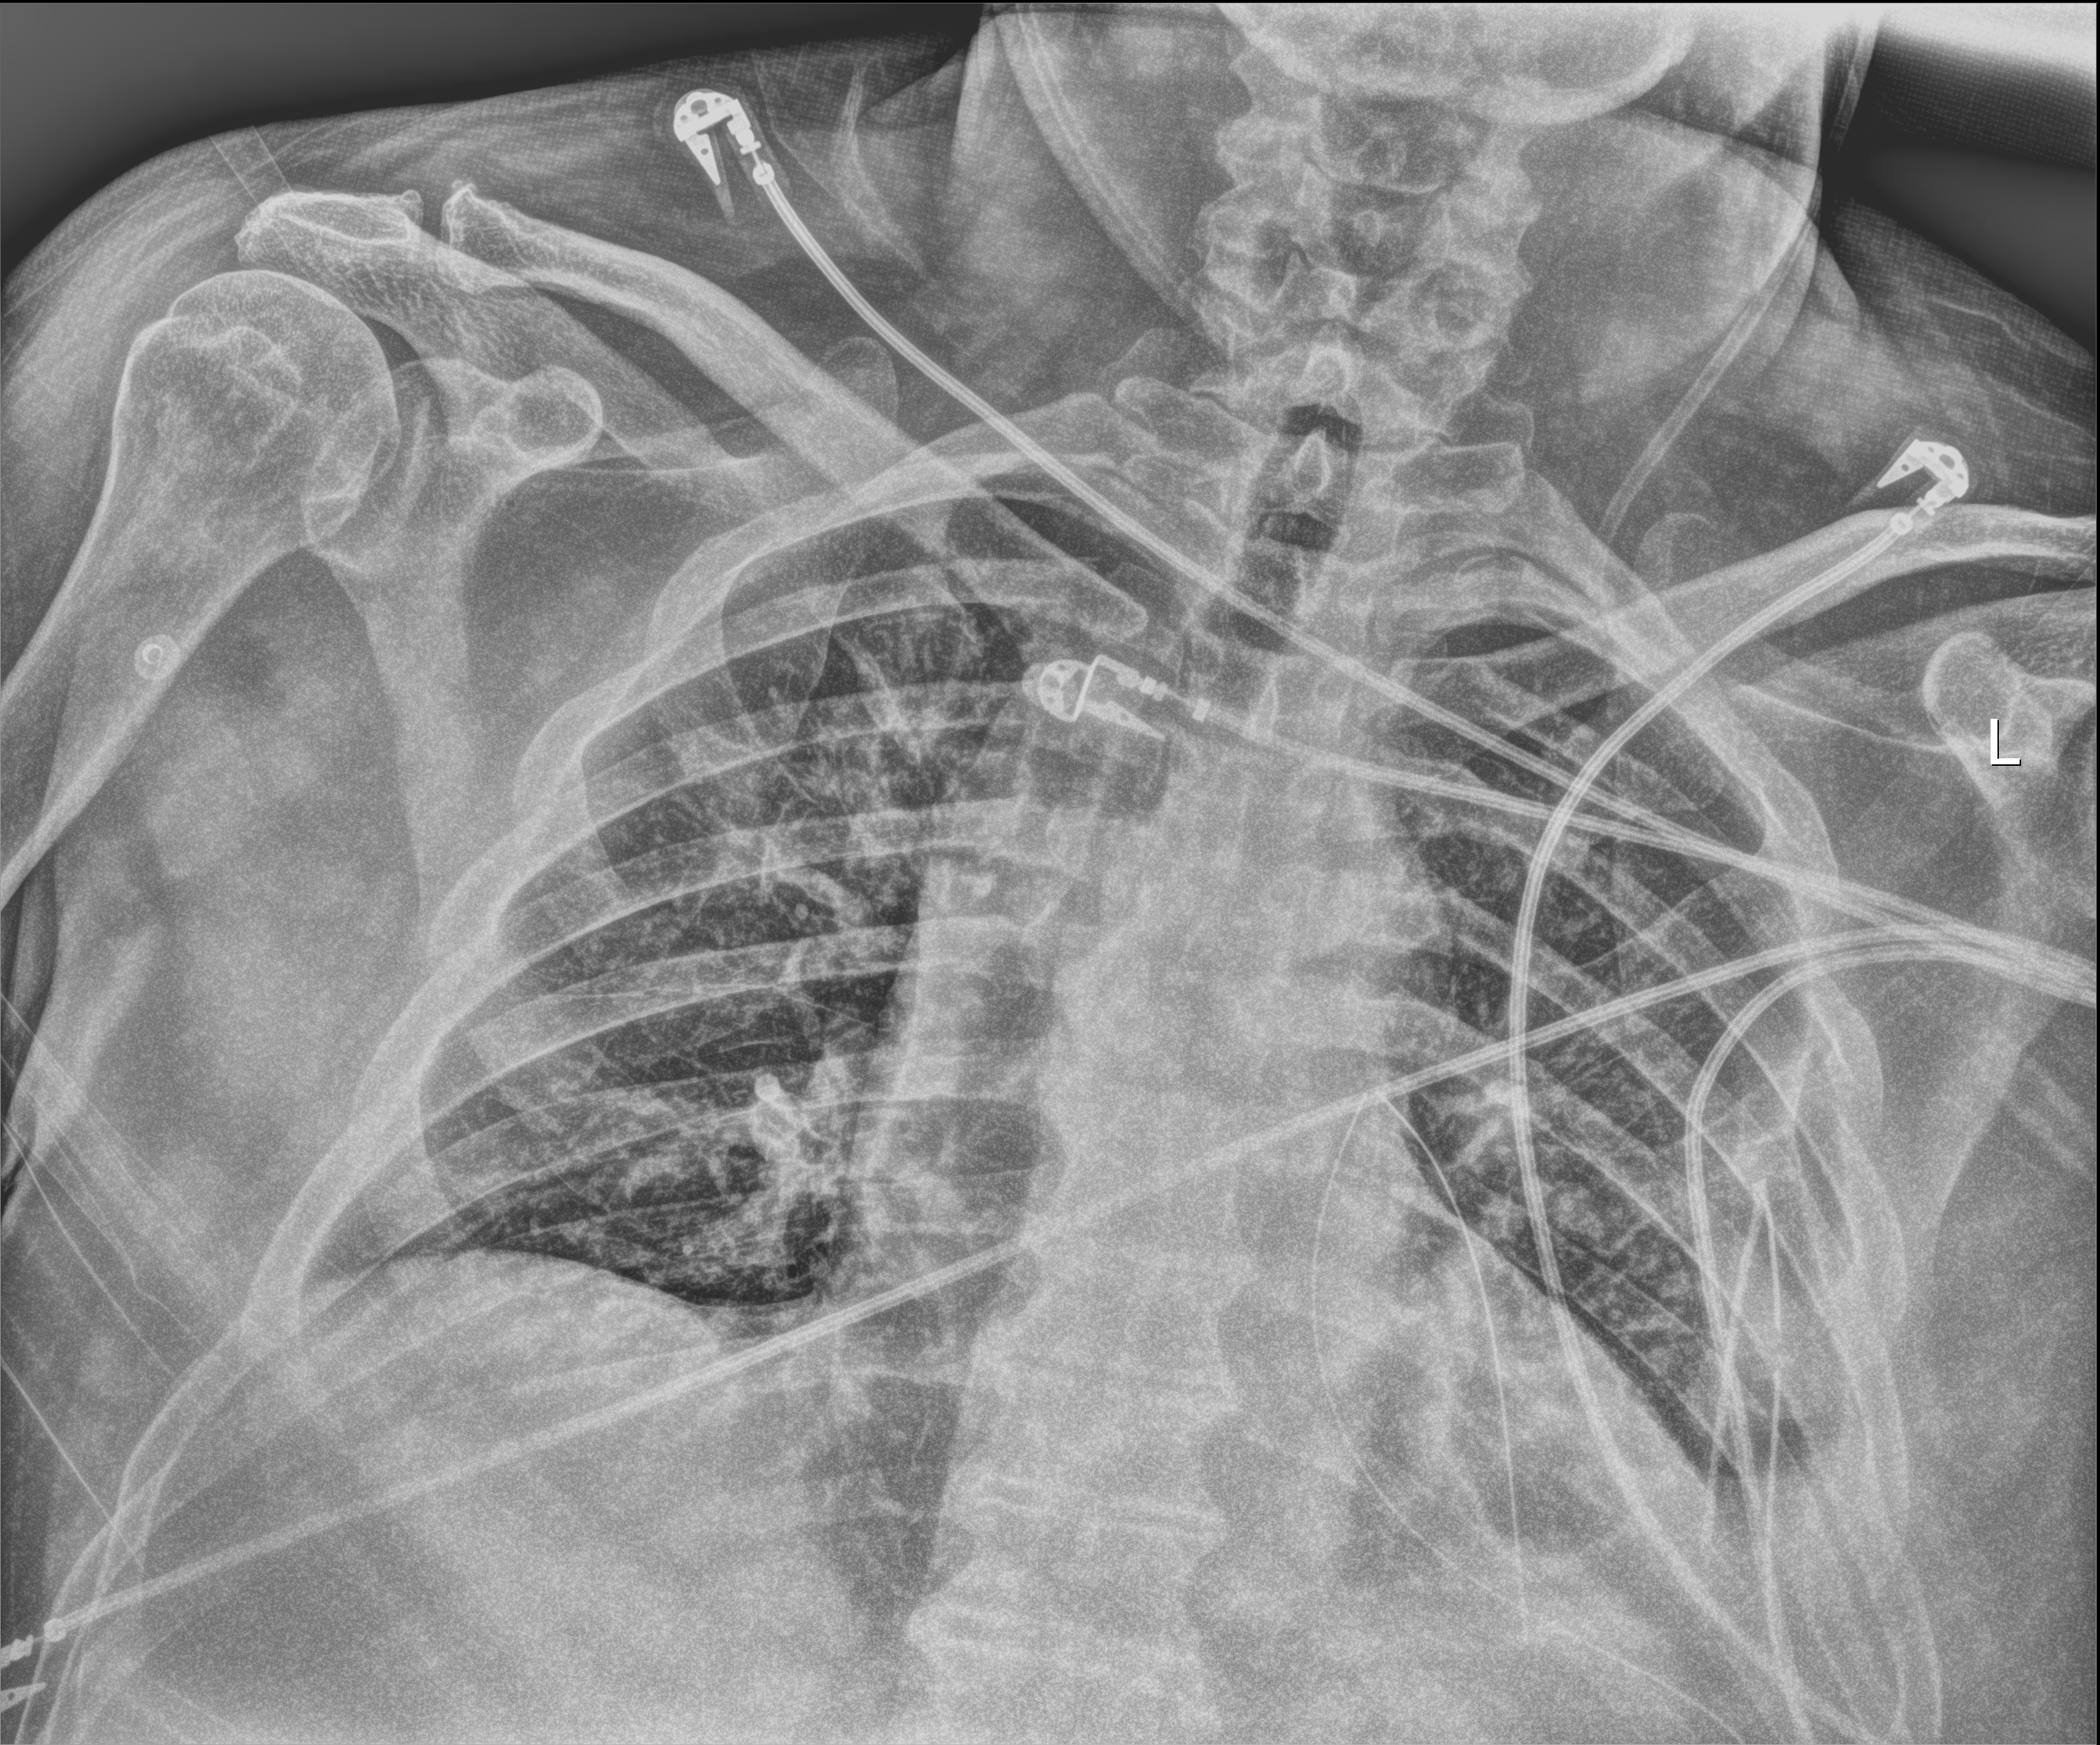
Bedside chest radiograph (digital radiography); anteroposterior (AP) projection. Patient hospitalised with COVID-19; male, aged 18–59 years.
Hospital-stay facts (about this admission, not read from this image; timing relative to this image not recorded): admitted to intensive care during this hospital stay: no; length of hospital stay: 10 days; mechanically ventilated during this hospital stay: no.